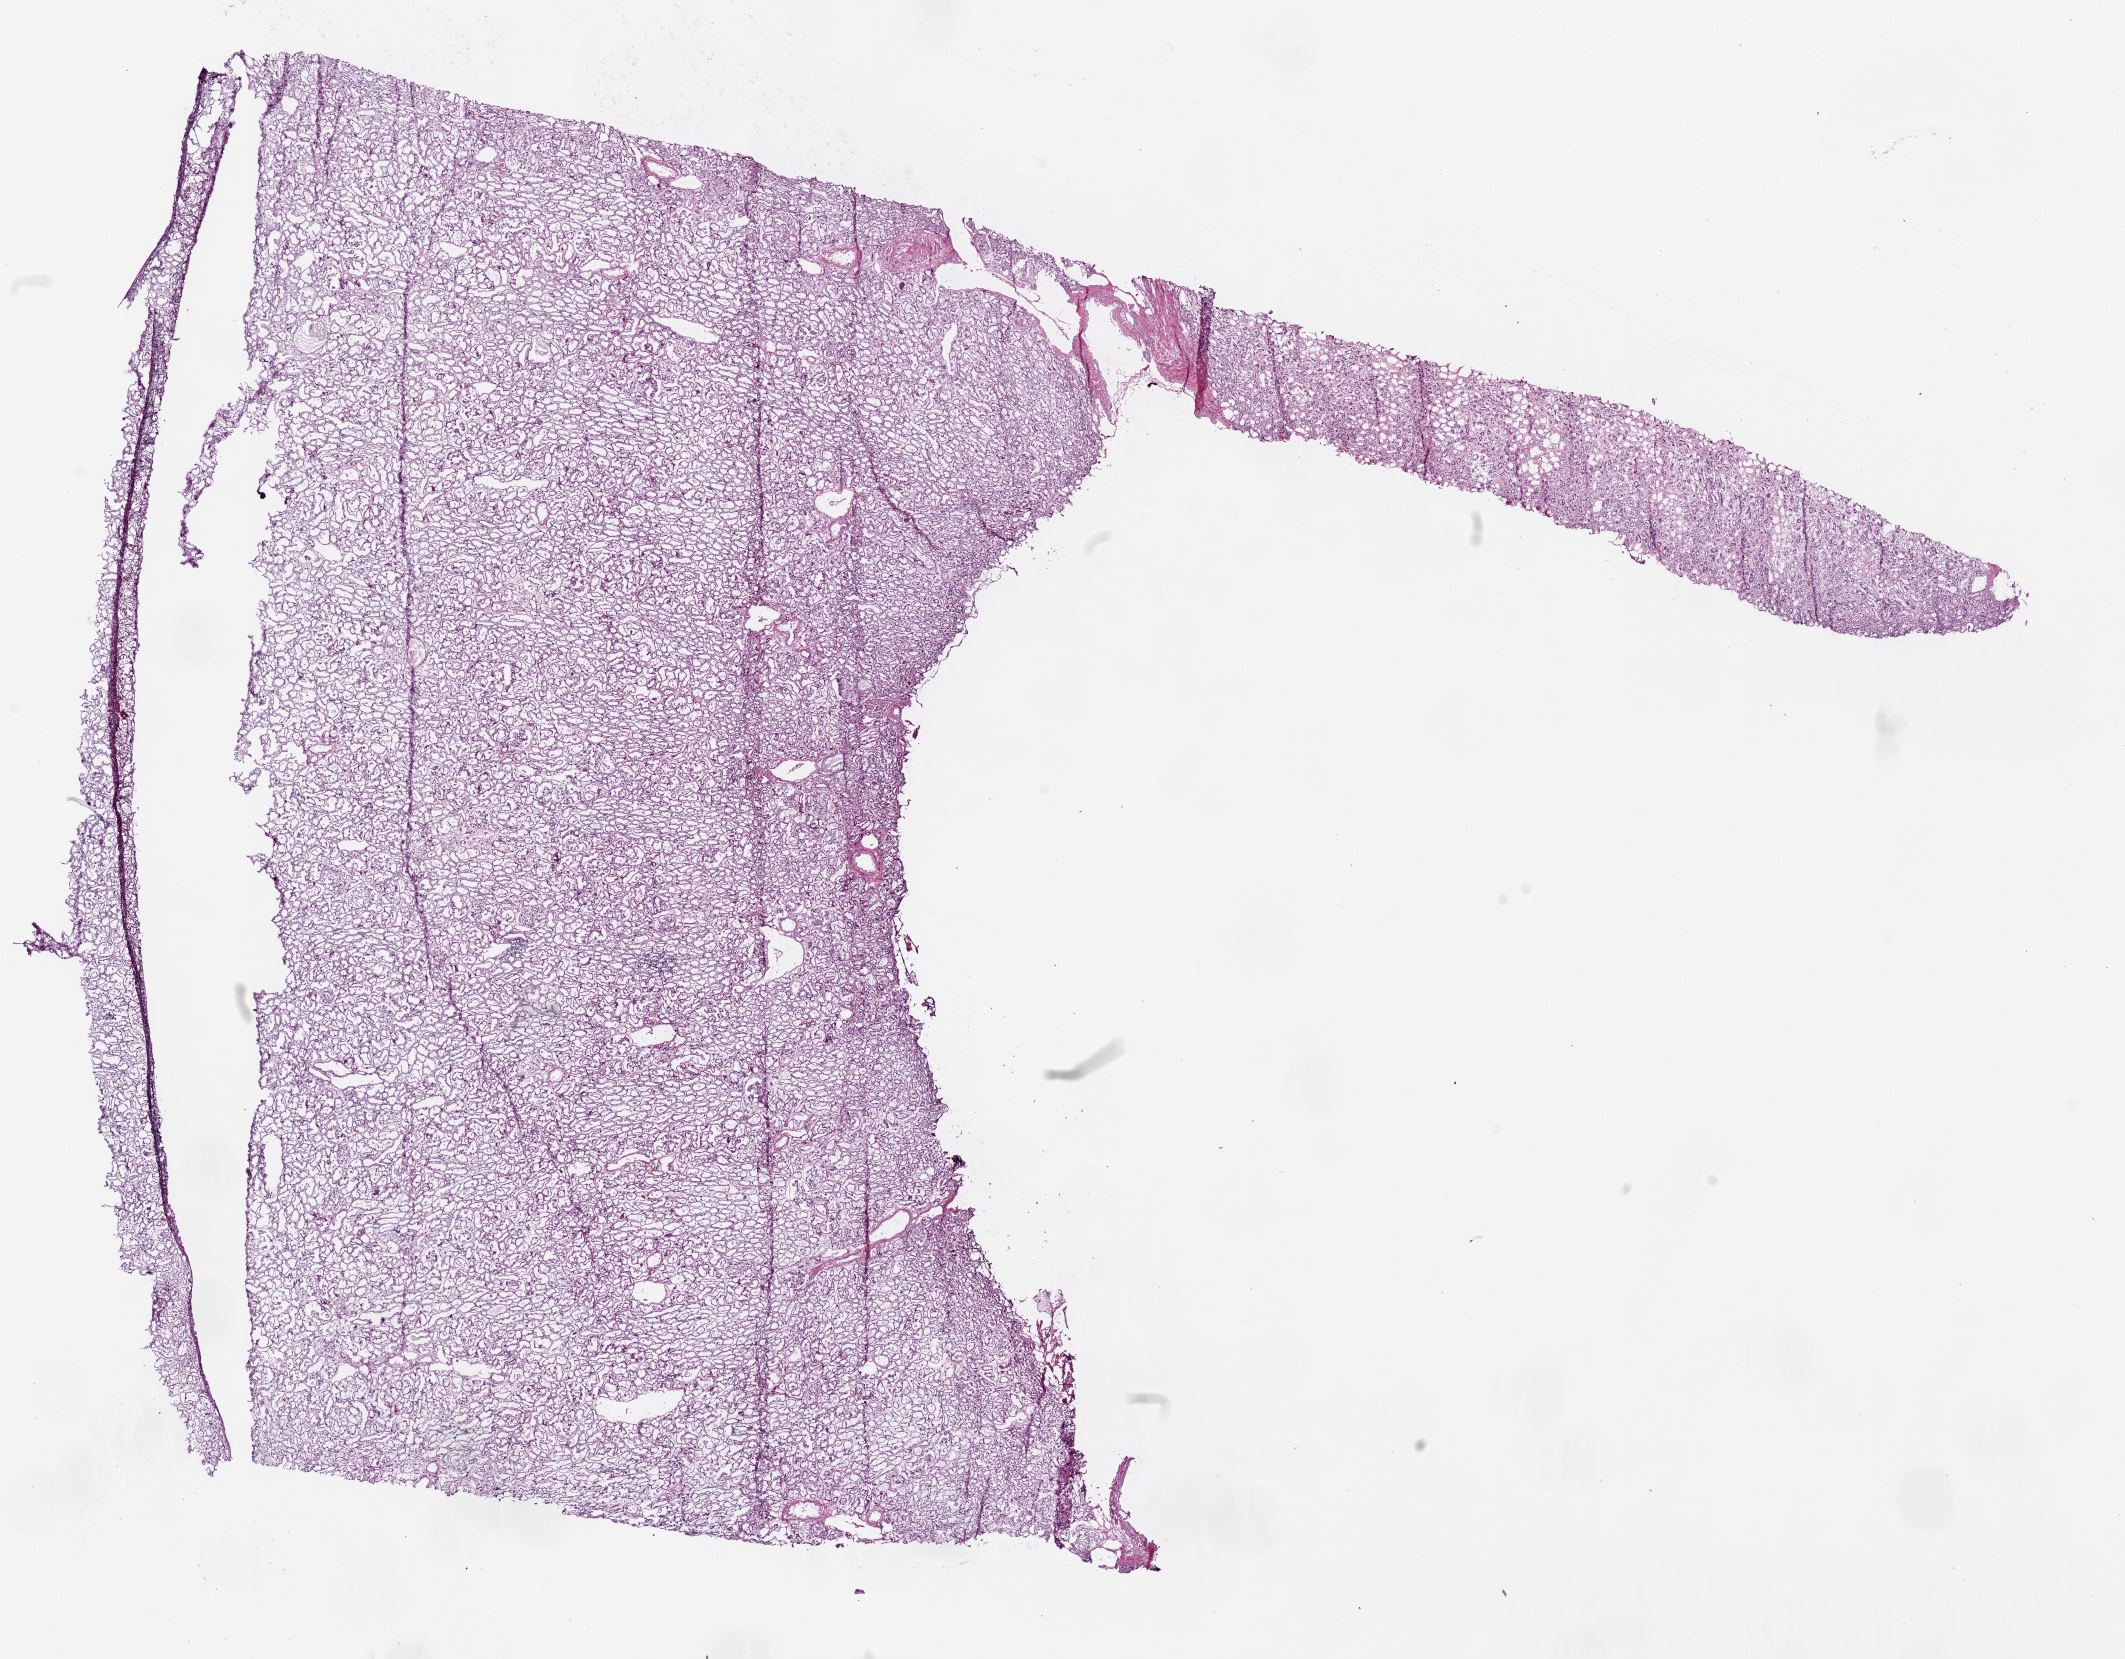
Whole-slide histology image, H&E-stained, low-resolution overview of the scanned area, about 17.1 x 13.3 mm. Frozen section. Sample: solid tissue normal (non-tumour tissue), kidney. Female patient; age at initial diagnosis 59 years.
This section: solid tissue normal sample (biorepository sample class). Patient diagnosis: Clear cell adenocarcinoma, NOS.